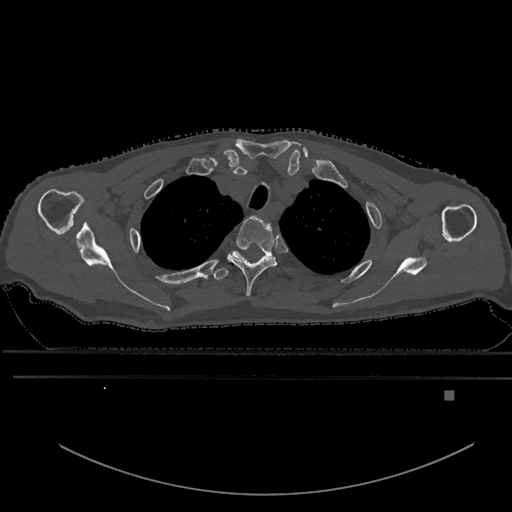
CT including the spine, one axial slice. Position 488 of 969 along the scan axis. Bone window (W 1800 / L 400 HU). 0.5 mm slice thickness. 512 × 512 image matrix, field of view 456 × 456 mm. Male patient, age 82 years. Case-level facts recorded for this patient, not image findings: primary cancer: prostate; vertebrae with lytic lesions (as recorded): T11, T9, T8, T2.
Outlined on this slice (semi-automatically segmented with operator editing):
- T2 vertebra: box from (x=227, y=215) to (x=277, y=298) px
- T3 vertebra: (x=212, y=252)–(x=245, y=281)